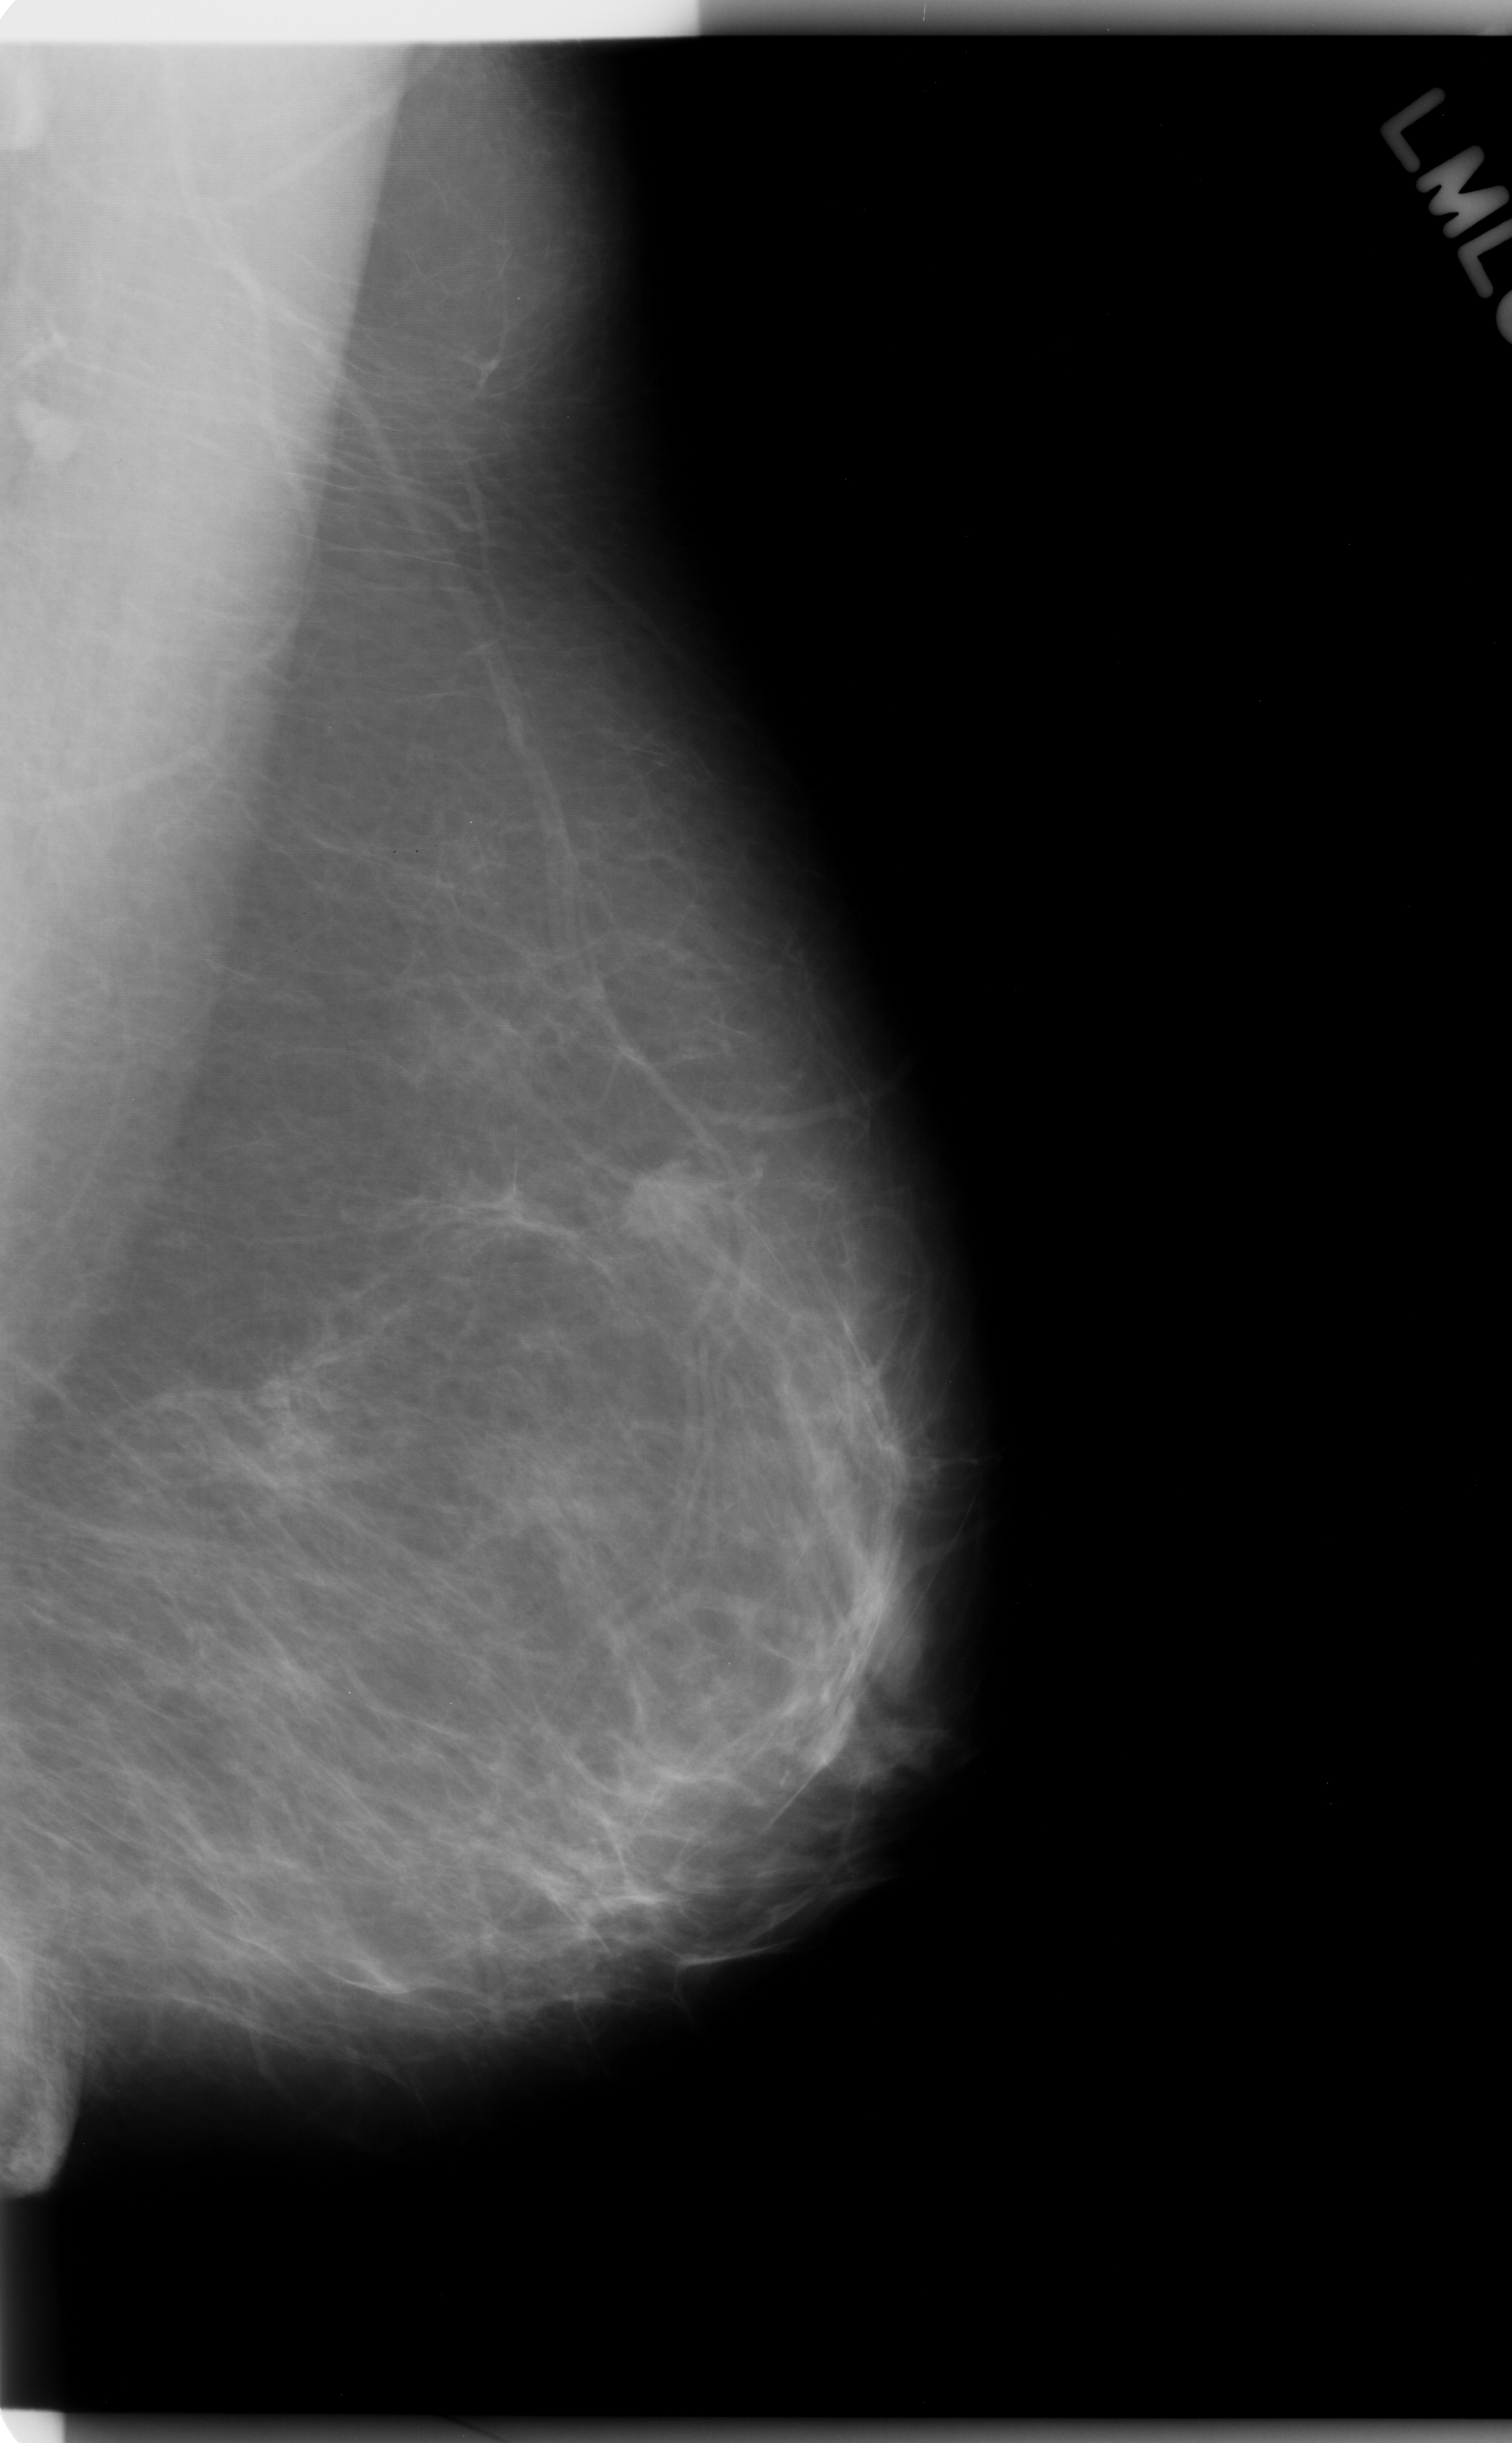
Scanned film-screen mammogram; left breast; mediolateral oblique (MLO) view; breast composition: almost entirely fatty (BI-RADS density category 1 of 4).
Radiologist-marked abnormalities on this image: mass, shape oval, margins spiculated; BI-RADS assessment category 5; pathology result (as recorded, not read from the image): malignant.